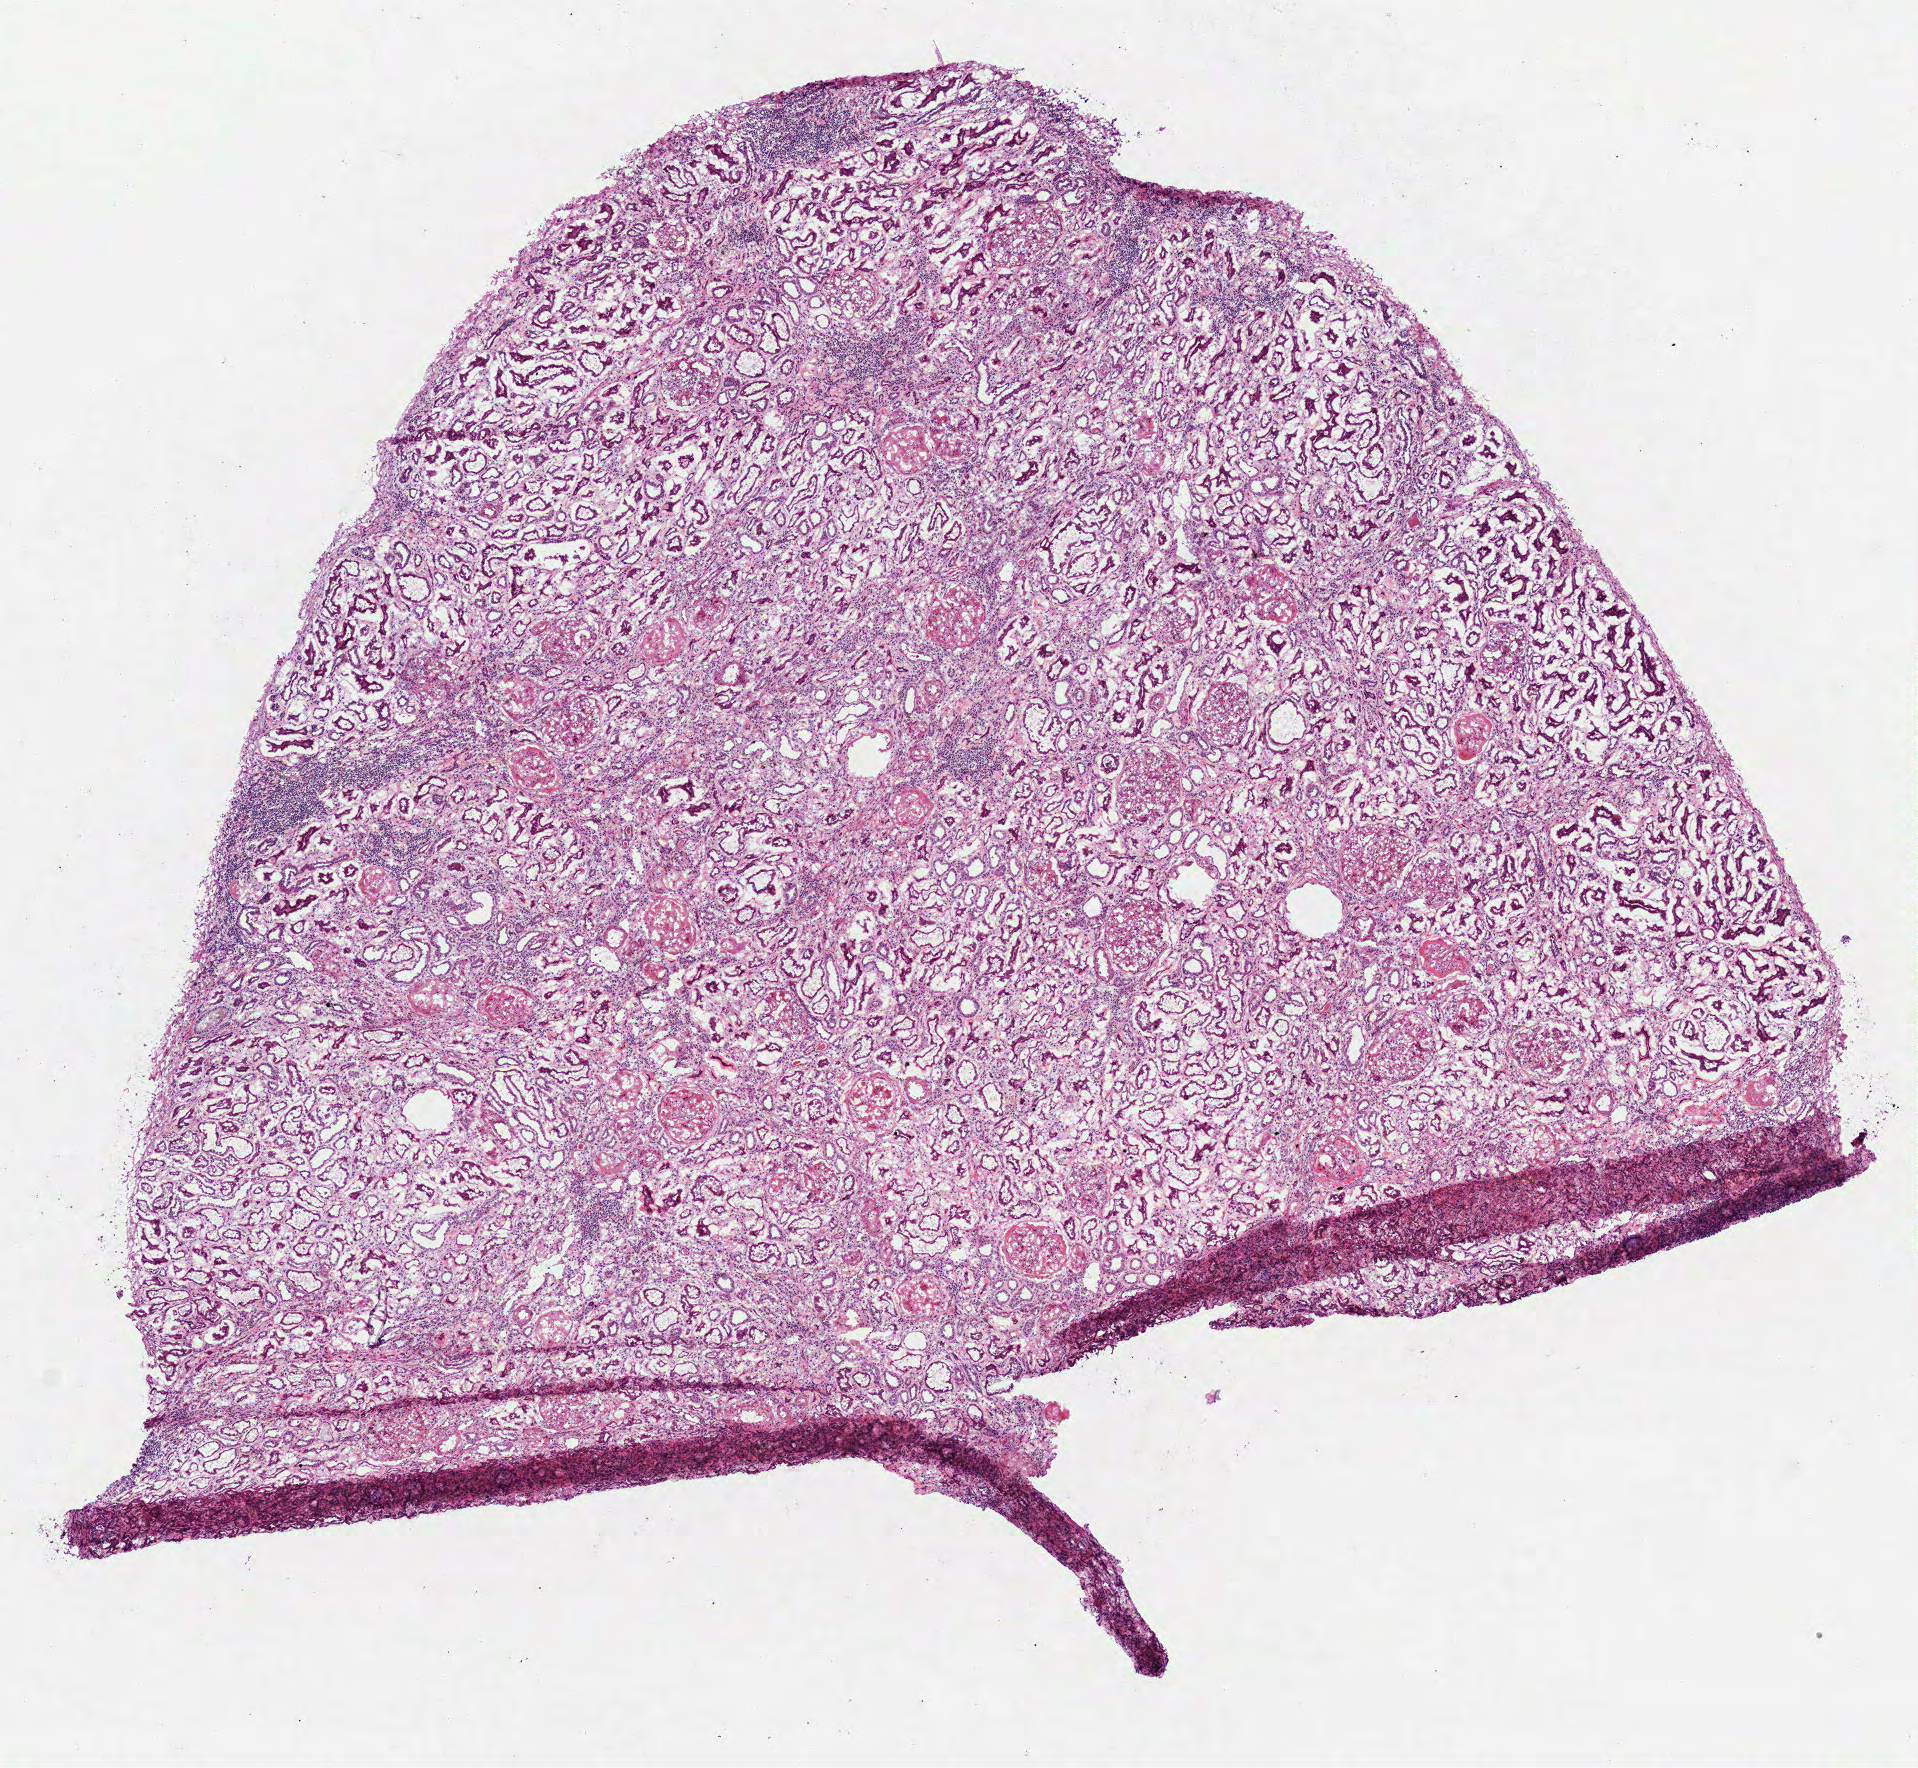
H&E whole-slide image, shown as a low-resolution overview of the whole scanned area (about 7.7 x 7.1 mm, acquisition: 40x scan), frozen section, sample: solid tissue normal (non-tumour tissue), kidney. Patient: male, age at initial diagnosis 48 years.
This section: solid tissue normal (non-tumour) sample from the same patient. Patient diagnosis: Papillary adenocarcinoma, NOS.